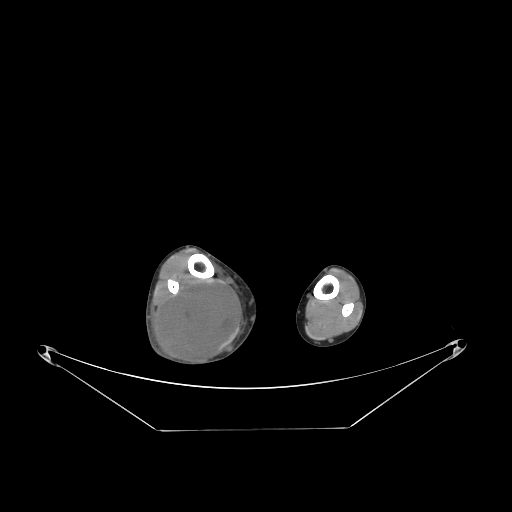
CT of an extremity soft-tissue mass (from a PET/CT study), one axial slice; position 72 of 267 along the scan axis; soft-tissue window (W 400 / L 40 HU); 512 × 512 image matrix, field of view 500 × 500 mm. Male patient. Case-level facts recorded for this patient, not image findings: histological type: liposarcoma - round cell; grade: high; site of the primary tumour: right calf.
Outlined on this slice (expert contour drawn on MRI and transferred to this co-registered scan by the dataset authors):
- gross tumour volume (mass): bounding box <157,279,241,366> (left, top, right, bottom; pixels)